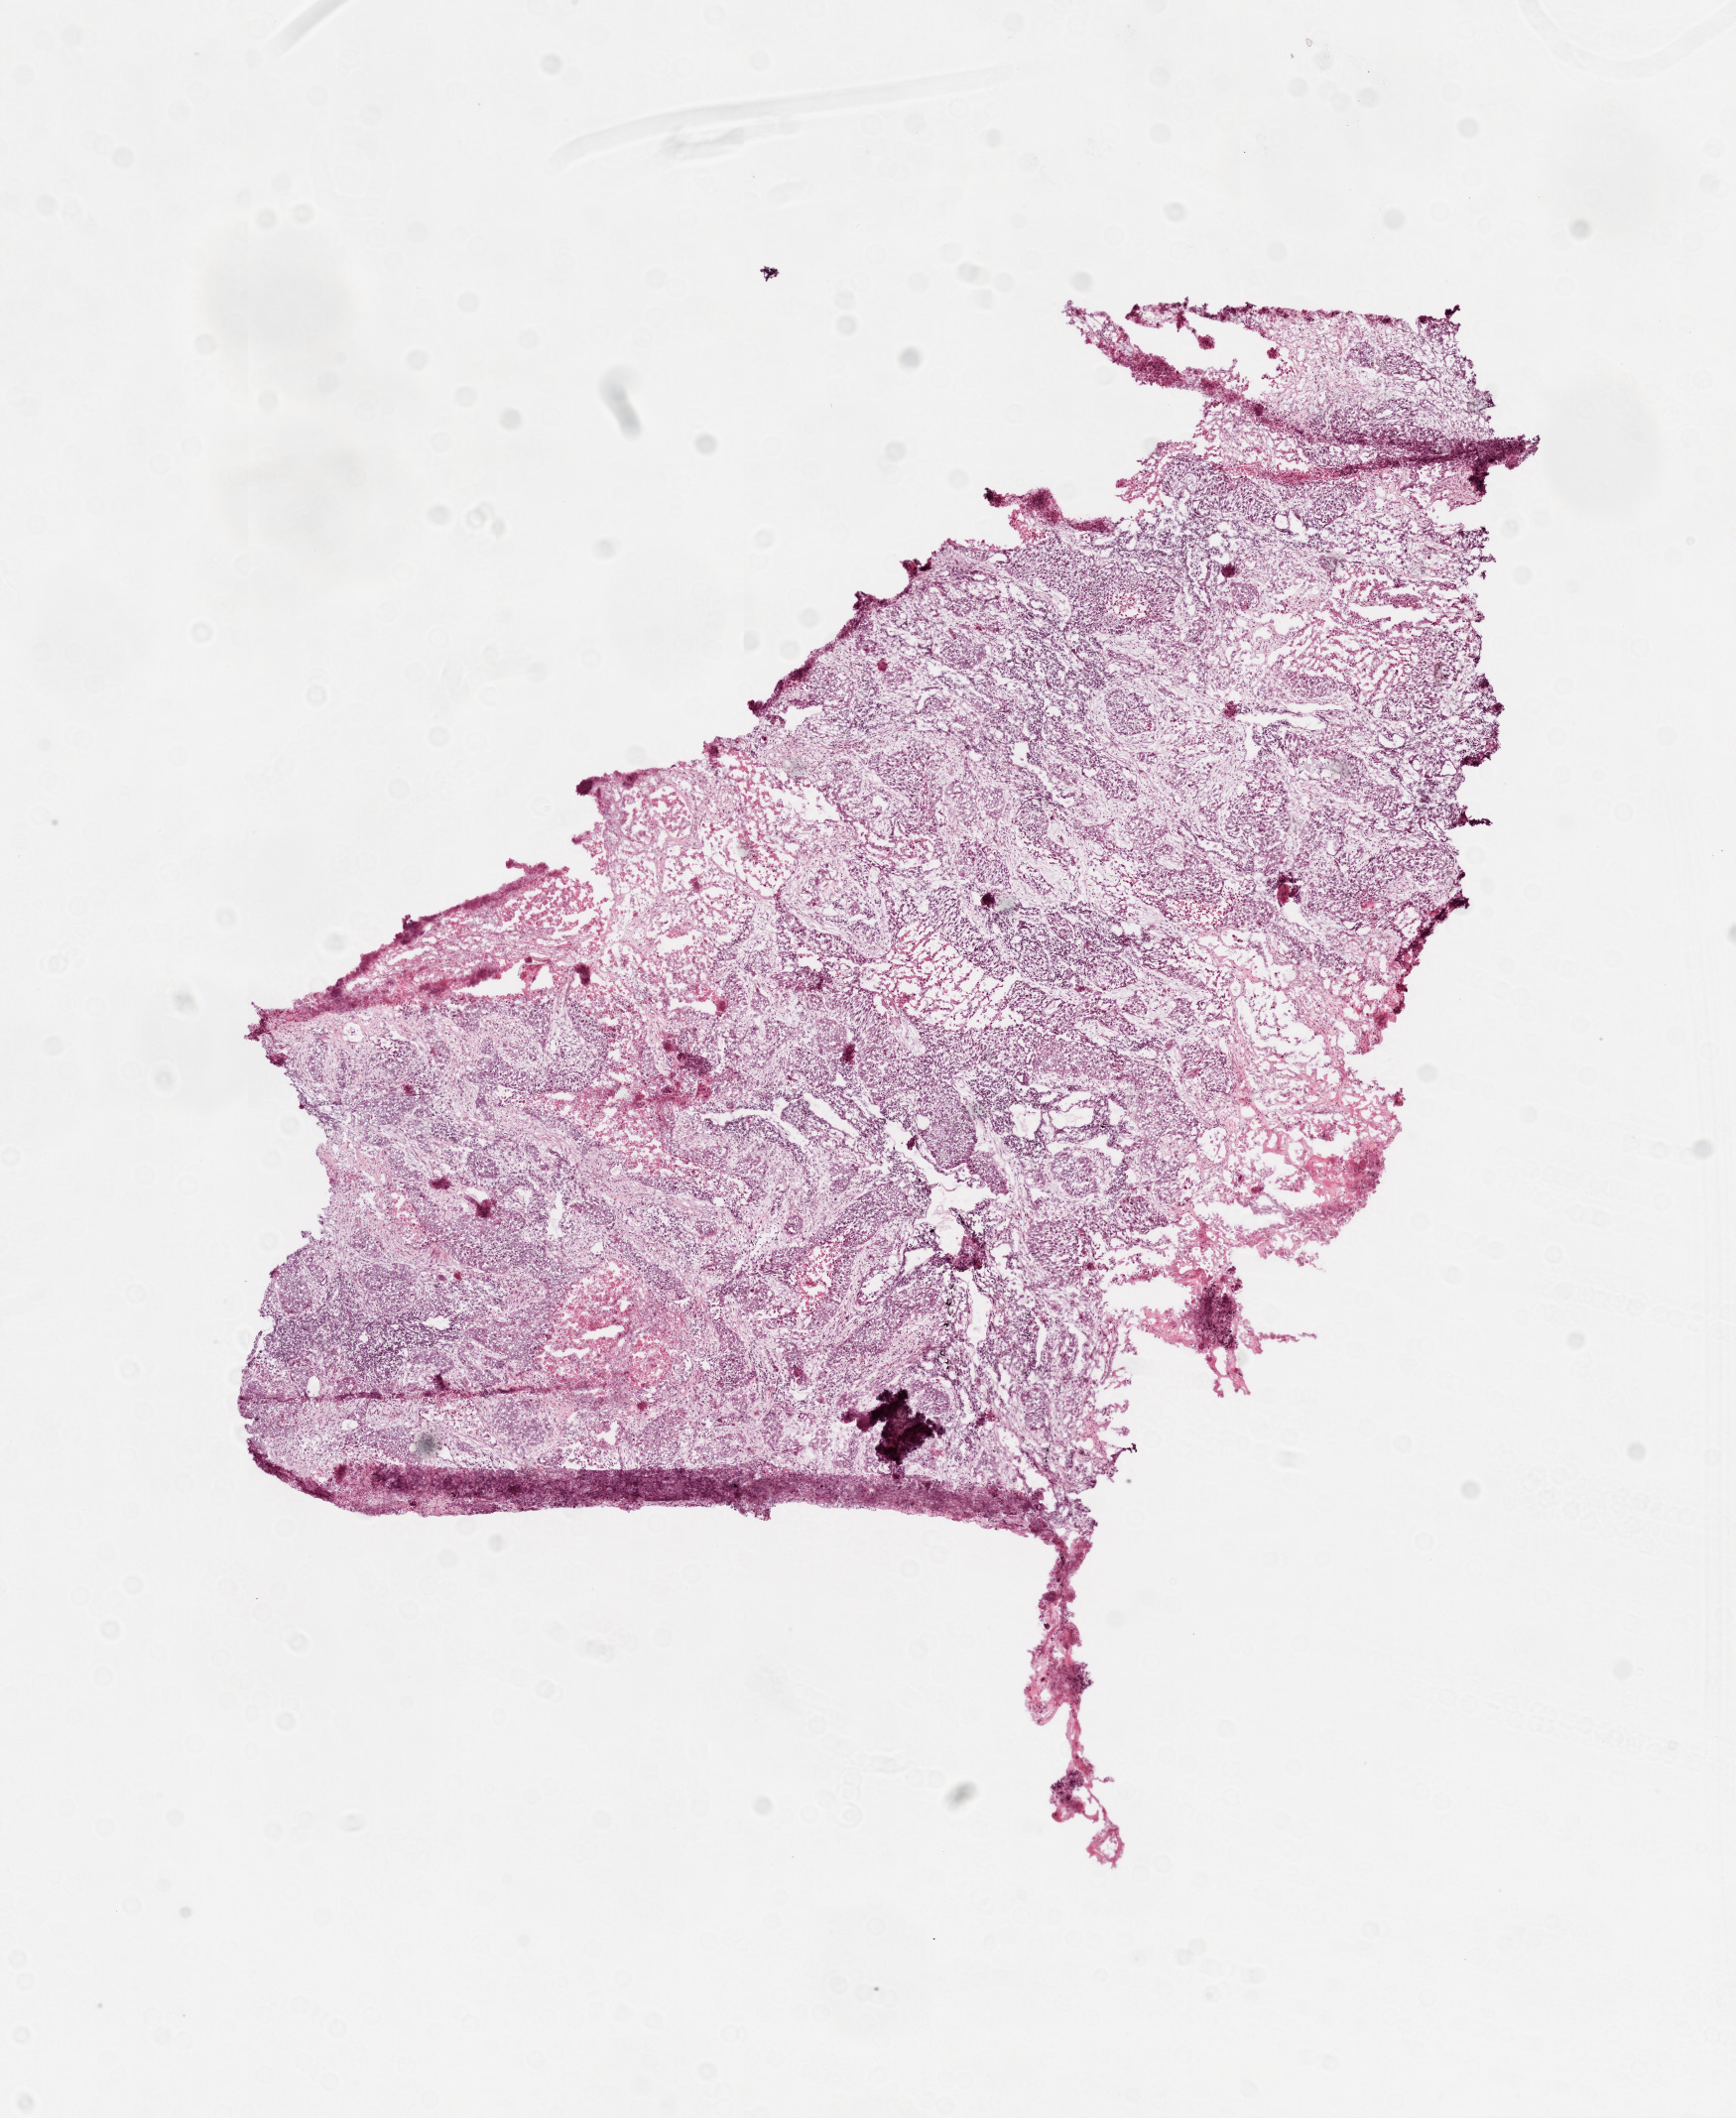
Whole-slide histology image, H&E, low-resolution overview of the scanned area, about 7.0 x 8.6 mm, frozen section from the top of the tissue portion, sample: primary tumour, lung. Patient: male, age at initial diagnosis 73 years. Slide review estimates, as recorded: tumour cells 60%, tumour nuclei 74%, normal cells 0%, stromal cells 10%, necrosis 30%.
* AJCC pathologic stage: IIB (5th edition)
* histologic diagnosis: Squamous cell carcinoma, NOS